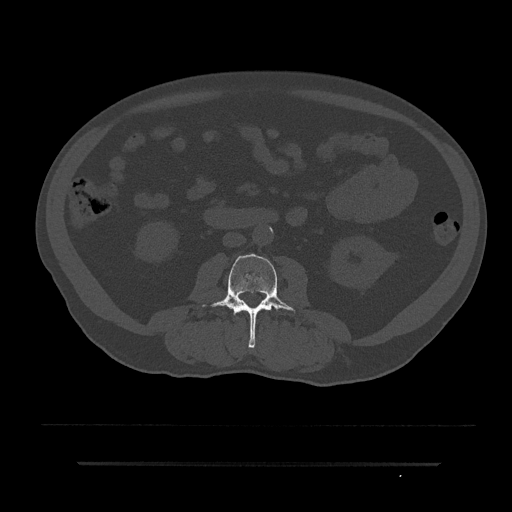
CT including the spine, one axial slice; slice 7 of 797 in the series (ordered by position); reconstruction kernel Br40s/3; 120 kVp; bone window (W 1800 / L 400 HU); 0.5 mm slice thickness; 512 × 512 image matrix, field of view 464 × 464 mm. Male patient, age 59 years. From the clinical record (not read from this slice): primary cancer: bile ducts.
Structures marked on this image (semi-automatically segmented with operator editing):
- L2 vertebra: box from (x=242, y=310) to (x=249, y=312) px
- L3 vertebra: (x=202, y=254)–(x=301, y=348)